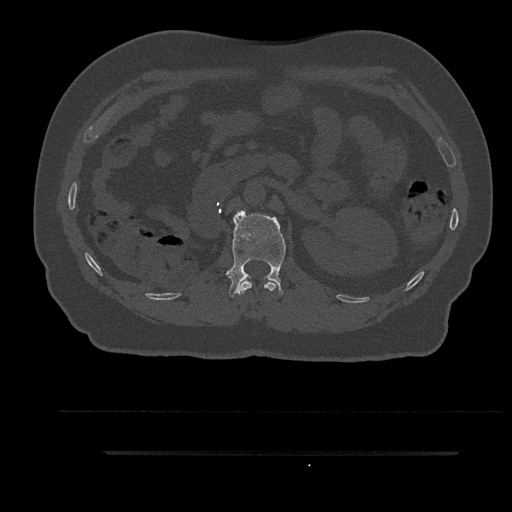
CT including the spine, one axial slice; slice 189 of 797 in the series (ordered by position); reconstruction kernel Br40s/3; 120 kVp; bone window (W 1800 / L 400 HU); 0.5 mm slice thickness; 512 × 512 image matrix, field of view 432 × 432 mm. Patient: male, 63 years. Case-level facts recorded for this patient, not image findings: primary cancer: renal; vertebrae with lytic lesions (as recorded): T8.
Outlined on this slice (semi-automatic segmentation, software-assisted and operator-edited):
- L1 vertebra: box from (x=226, y=209) to (x=286, y=298) px
- T12 vertebra: (x=240, y=280)–(x=278, y=294)